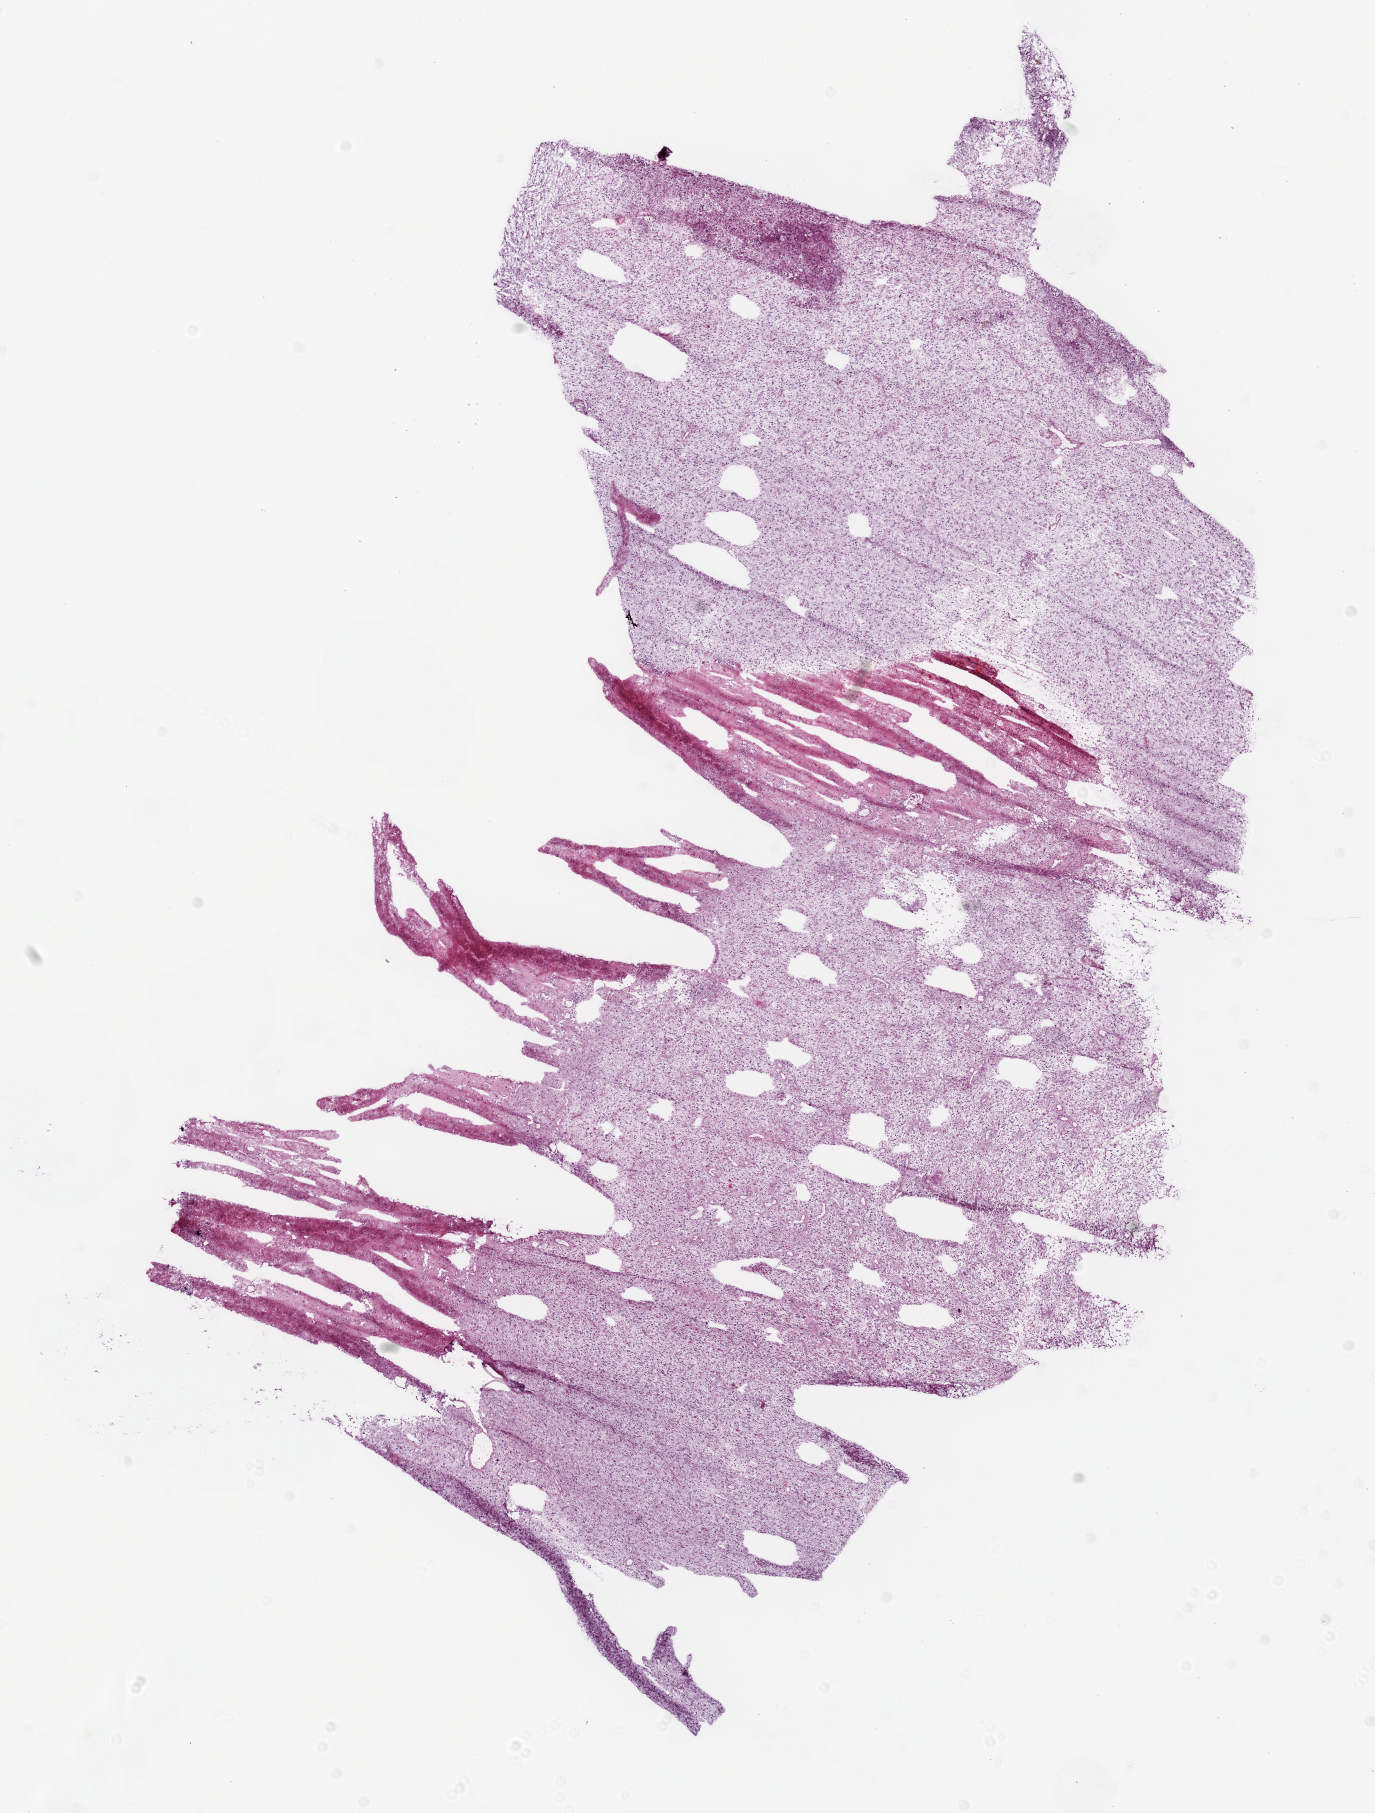
Digitized H&E tissue section (whole slide) — whole scanned area (about 11.0 x 14.5 mm) shown as a low-resolution overview, frozen section from the bottom of the tissue portion, brain, primary tumour sample. Female patient; age at initial diagnosis 28 years. Composition of this section per pathologist review: tumour cells 80%, tumour nuclei 90%, normal cells 10%, stromal cells 10%, necrosis 0%.
Diagnosis: Glioblastoma.